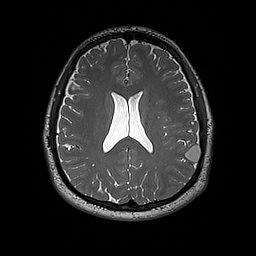
Brain MRI from a brain-tumour surgery series, one axial slice; slice 82 of 192 in the series (ordered by position); 1 mm slice thickness; 256 × 256 image matrix. From the clinical record (not read from this slice): histopathology: Dysembryoplastic neuroepithelial tumor; WHO grade: 1; IDH mutation: no; tumour location: Left Inferior Parietal.
Outlined on this slice (manually delineated by an expert):
- tumour: bounding box <186,146,201,162> (left, top, right, bottom; pixels)